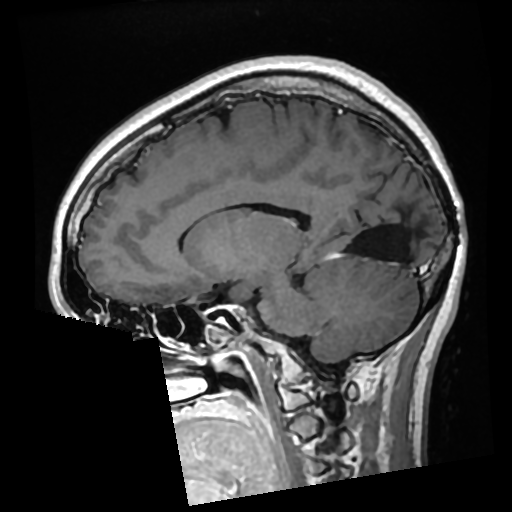
Brain MRI from a brain-tumour surgery series, one sagittal slice; position 121 of 276 along the scan axis; T1-weighted post-contrast; 0.7 mm slice thickness; 512 × 512 image matrix. From the clinical record (not read from this slice): histopathology: Glioma with ependymal features; WHO grade: 2; tumour location: Left Parietal.
Annotated regions visible in this slice (expert manual segmentation):
- previous resection cavity: bounding box <349,206,406,260> (left, top, right, bottom; pixels)